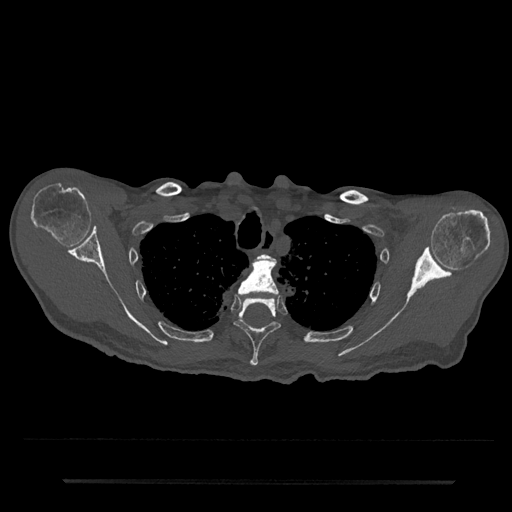
CT including the spine, one axial slice; position 629 of 797 along the scan axis; reconstruction kernel Br40s/3; 120 kVp; bone window (W 1800 / L 400 HU); 512 × 512 image matrix, field of view 427 × 427 mm. Patient: male, 74 years. From the clinical record (not read from this slice): primary cancer: prostate.
Annotated regions visible in this slice (semi-automatically segmented with operator editing):
- T2 vertebra: box from (x=258, y=254) to (x=271, y=260) px
- T3 vertebra: (x=238, y=256)–(x=279, y=295)
- T4 vertebra: (x=234, y=298)–(x=281, y=366)